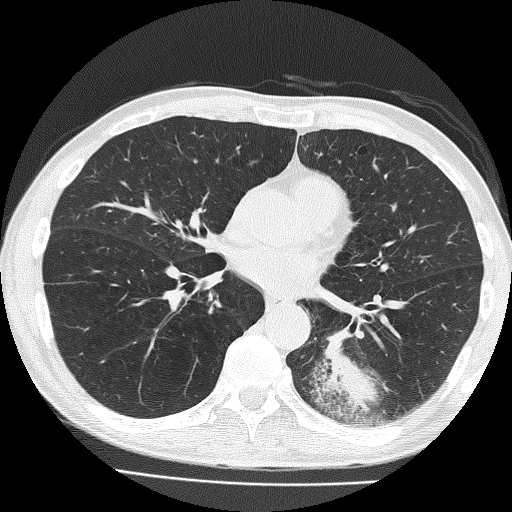
Axial slice from a low-dose chest CT screening exam. Baseline screening round. Lung window (W 1500 / L -600 HU). Lung (sharp) reconstruction kernel (FC51). 512 × 512 image matrix, field of view 324 × 324 mm. Male, age 58 years at enrolment. Current smoker at enrolment.
Expert-annotated lung lesion, bounding box (x1, y1, x2, y2) in pixels: (303, 315, 418, 434). The screening reader recorded 2 non-calcified nodules or masses ≥4 mm on this exam (left lower lobe, left upper lobe); which of them this box marks is not recorded. Official screen result: positive, change unspecified: nodule(s) >= 4 mm or enlarging nodule(s), mass(es), or other non-specific abnormalities suspicious for lung cancer. Participant outcome: lung cancer diagnosed 39 days after this screen — non-small cell carcinoma, left lower lobe, poorly differentiated (G3), stage IV (AJCC 6th edition), 74 mm at pathology.